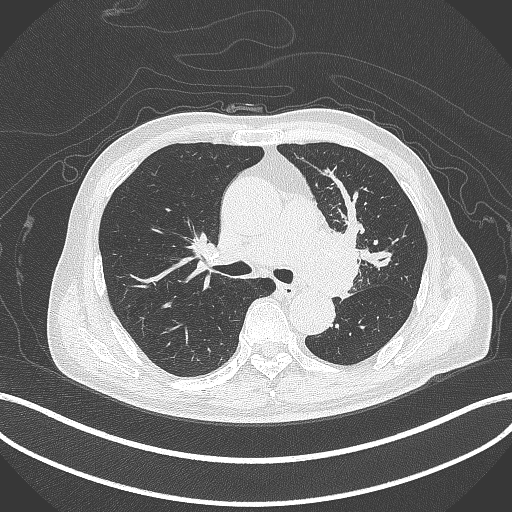
Chest CT, one axial slice. Position 269 of 417 along the scan axis. 120 kVp. Lung window (W 1500 / L -600 HU). 512 × 512 image matrix, field of view 400 × 400 mm. Male patient, age 77 years. Case-level facts recorded for this patient, not image findings: clinical TNM (as recorded): T3 N1 M0.
Outlined on this slice (rectangle marked by the reading radiologist):
- lung tumour (recorded histology: adenocarcinoma): box from (x=314, y=221) to (x=366, y=300) px